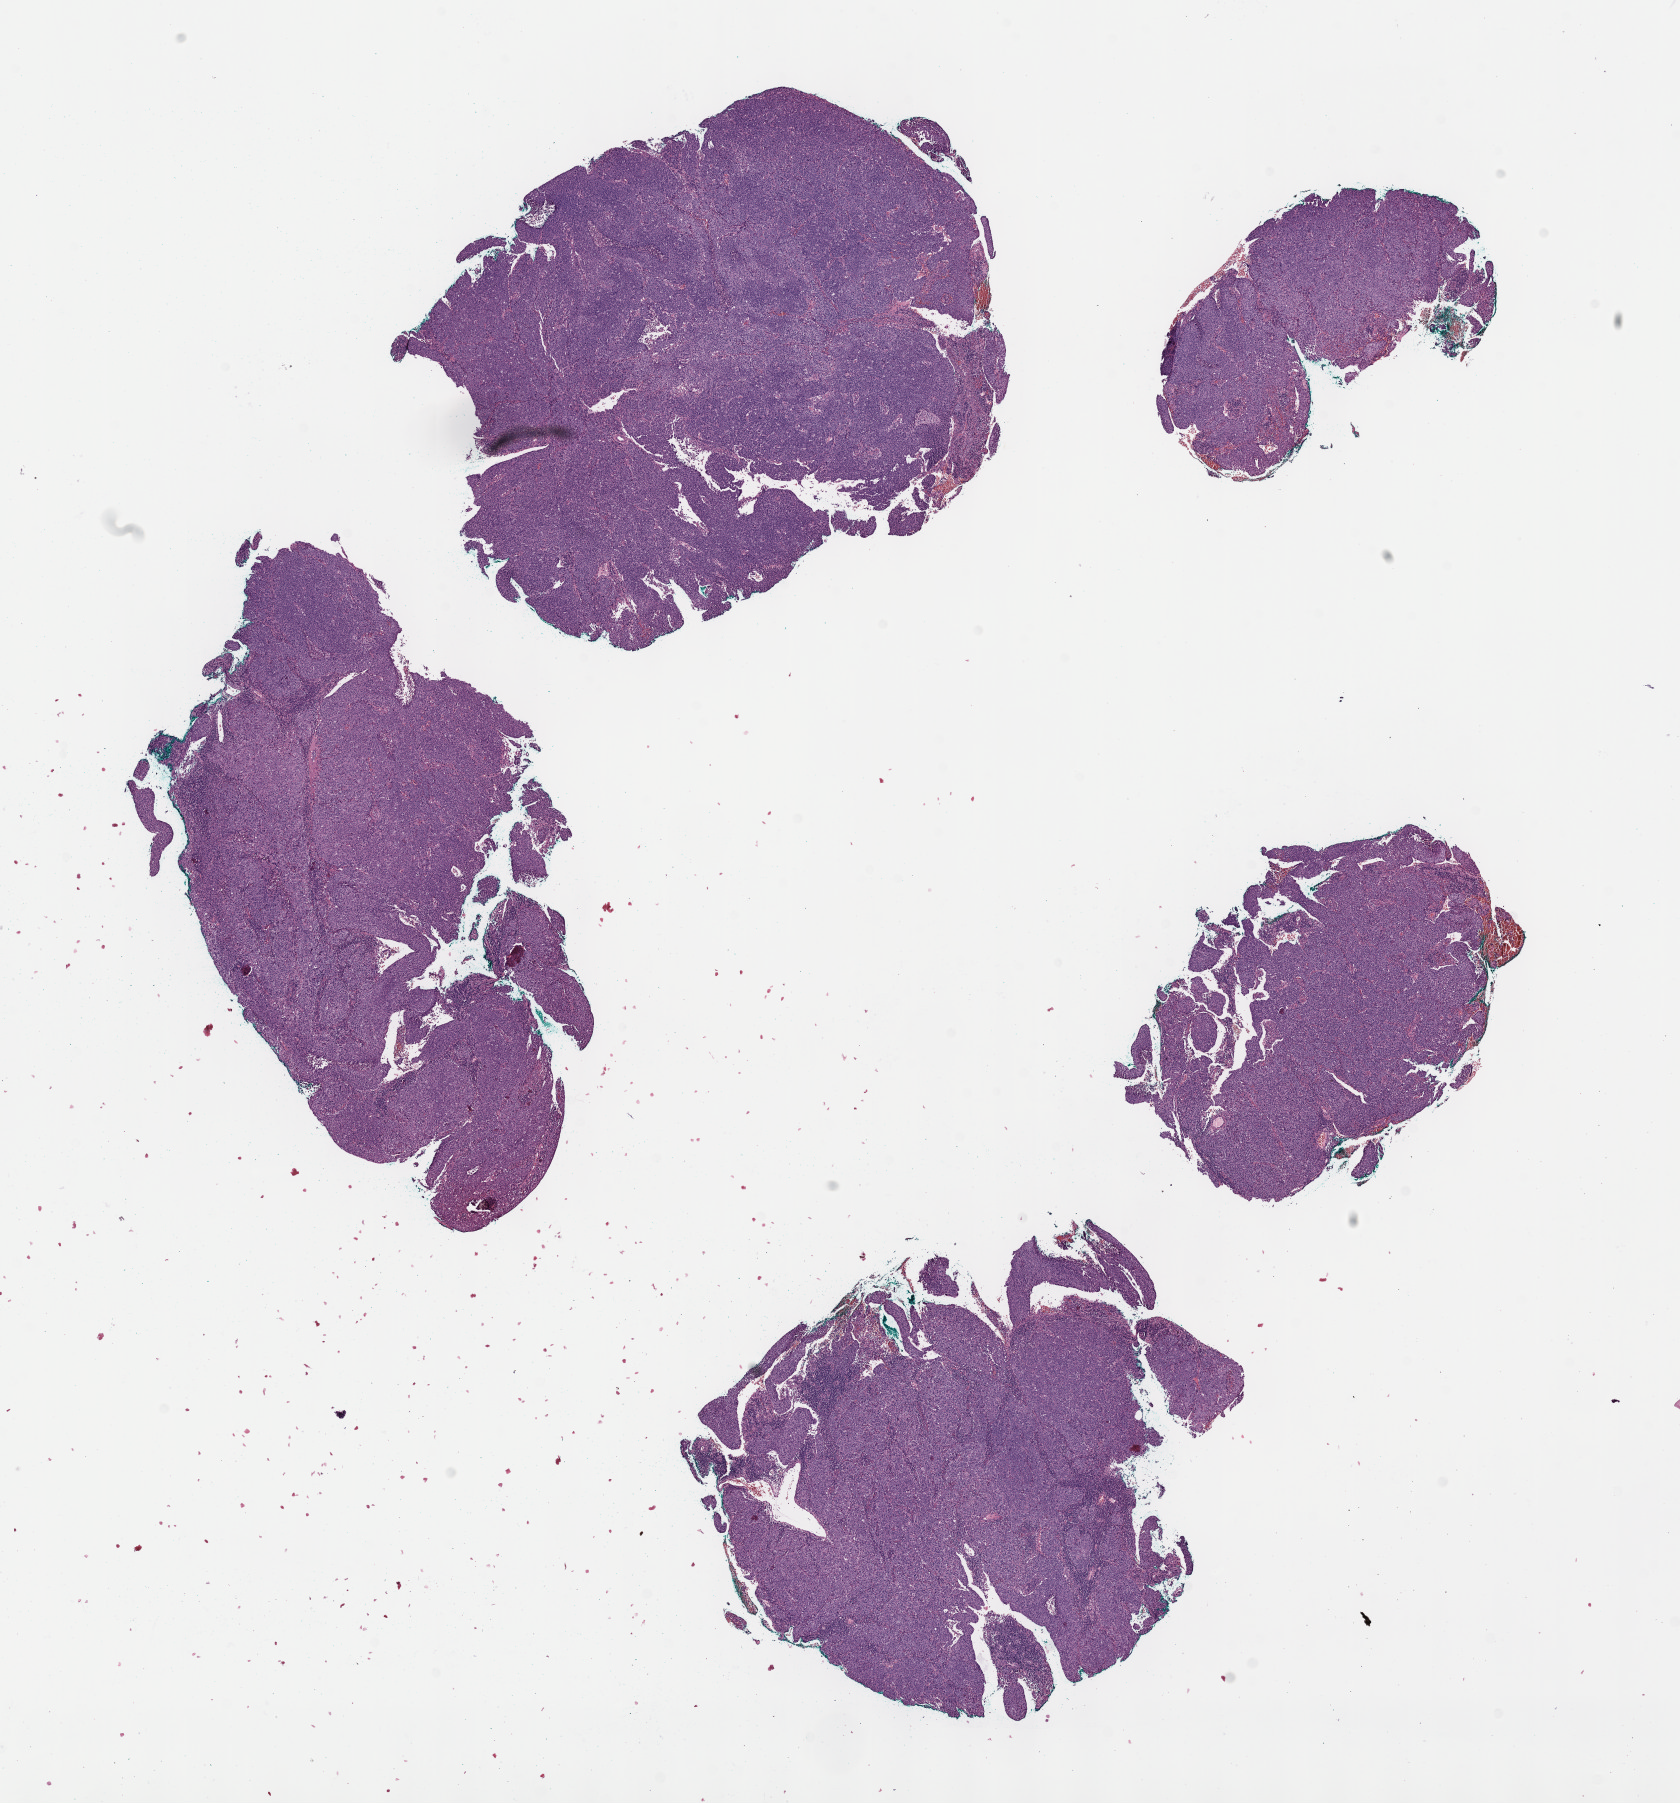
Whole-slide histology image, H&E-stained, shown as a low-resolution overview of the whole scanned area (about 13.6 x 14.6 mm); formalin-fixed paraffin-embedded (FFPE) diagnostic section; sample: primary tumour, cervix. Female, age 46 years at initial diagnosis. Histologic grade: G2 (moderately differentiated).
Pathologic diagnosis: Squamous cell carcinoma, large cell, nonkeratinizing, NOS (cervix uteri). FIGO stage: IIB.